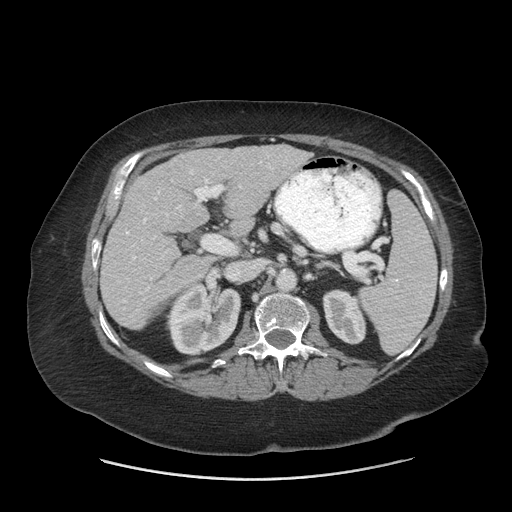
Contrast-enhanced abdominal CT (liver protocol), one axial slice. Position 33 of 69 along the scan axis. Soft-tissue window (W 400 / L 40 HU). 2.5 mm slice thickness. 512 × 512 image matrix. Case-level facts recorded for this patient, not image findings: diagnosis: hepatocellular carcinoma (patient treated with transarterial chemoembolisation; whether this scan precedes or follows treatment is not stated here); TNM stage (as recorded): Stage-IIIB; Child-Pugh class: A; tumour differentiation: moderately differentiated; tumour nodularity: multinodular.
Outlined on this slice (semi-automatic segmentation, software-assisted and operator-edited):
- liver parenchyma outside the tumour (the mass and vessels are separate outlines, so this box may not span the whole liver): box from (x=100, y=144) to (x=310, y=328) px
- liver vessels: (x=123, y=156)–(x=269, y=302)